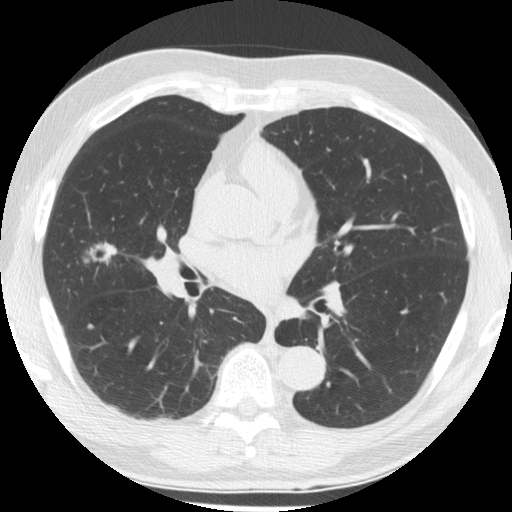
Low-dose screening chest CT, one axial slice. Slice 98 of 176 in the series (ordered by position). 120 kVp. Lung window (W 1500 / L -600 HU). 2.5 mm slice thickness. 512 × 512 image matrix, field of view 348 × 348 mm.
Structures marked on this image (expert manual segmentation):
- lesion 1 (tumor, middle lobe of right lung): box from (x=84, y=242) to (x=117, y=265) px